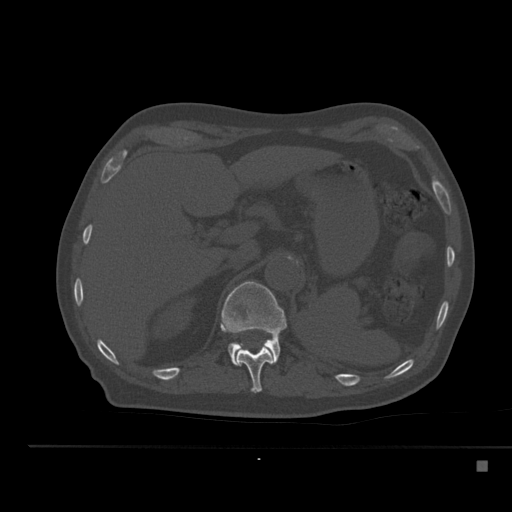
CT including the spine, one axial slice. Position 240 of 517 along the scan axis. Reconstruction kernel Br40s. Bone window (W 1800 / L 400 HU). 1.5 mm slice thickness. 512 × 512 image matrix, field of view 408 × 408 mm. Male patient, age 70 years. From the clinical record (not read from this slice): primary cancer: renal; vertebrae with lytic lesions (as recorded): T4, T6, T10, T12, L3, L4, L5.
Structures marked on this image (semi-automatically segmented with operator editing):
- T11 vertebra: box from (x=237, y=347) to (x=273, y=393) px
- T12 vertebra: (x=220, y=281)–(x=287, y=366)